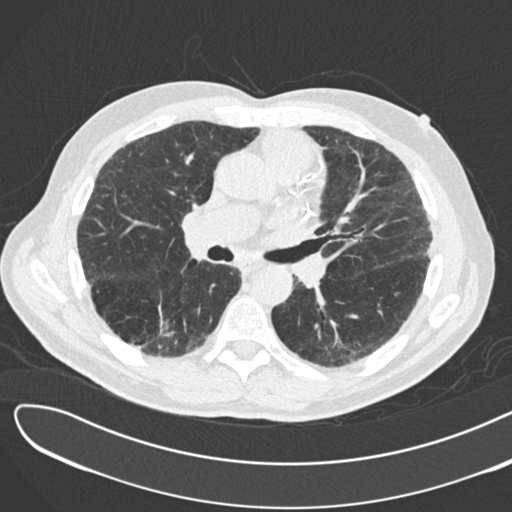
Axial slice from a low-dose chest CT screening exam, second screening round (one year after baseline), lung window (W 1500 / L -600 HU), 2 mm slice thickness, slice 89 of 183 in the series. Male participant, aged 72 years at enrolment. Former smoker at enrolment.
- Expert reader's lesion annotation, bounding box <138,292,193,347> (left, top, right, bottom; pixels).
- The screening reader recorded 2 non-calcified nodules or masses ≥4 mm on this exam (right lower lobe, right lower lobe); which of them this box marks is not recorded.
- Official screen result: positive, change unspecified: nodule(s) >= 4 mm or enlarging nodule(s), mass(es), or other non-specific abnormalities suspicious for lung cancer.
- Lung cancer was diagnosed 46 days after this screen: squamous cell carcinoma, NOS, right lower lobe, poorly differentiated (G3), stage IB (AJCC 6th edition), 42 mm at pathology.